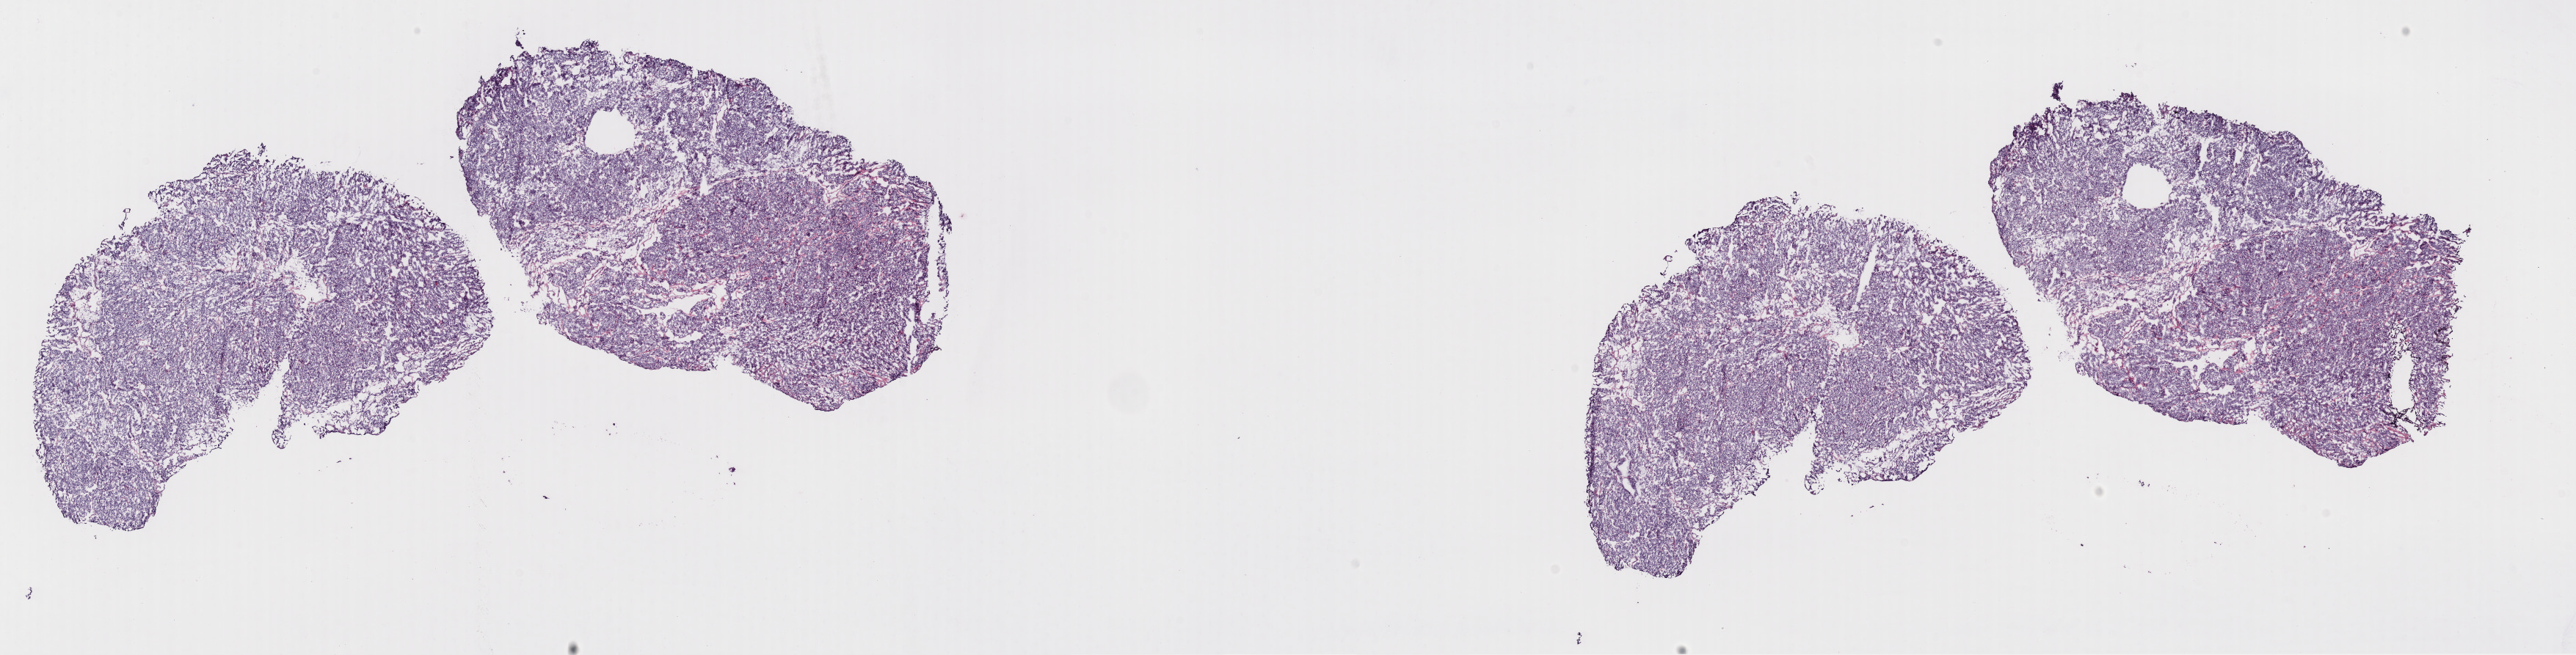
Digitized H&E tissue section (whole slide), whole scanned area (about 27.7 x 7.1 mm) shown as a low-resolution overview, frozen section from the top of the tissue portion, primary tumour sample from the thyroid. Female, age 33 years at initial diagnosis. Composition of this section per pathologist review: tumour cells 100%, tumour nuclei 80%, normal cells 0%, stromal cells 0%, necrosis 0%. Inflammatory infiltration, as recorded: lymphocyte infiltration 2%, monocyte infiltration 1%, neutrophil infiltration 0%.
Diagnosis: Papillary carcinoma, follicular variant (thyroid gland). AJCC pathologic stage: I (7th edition).